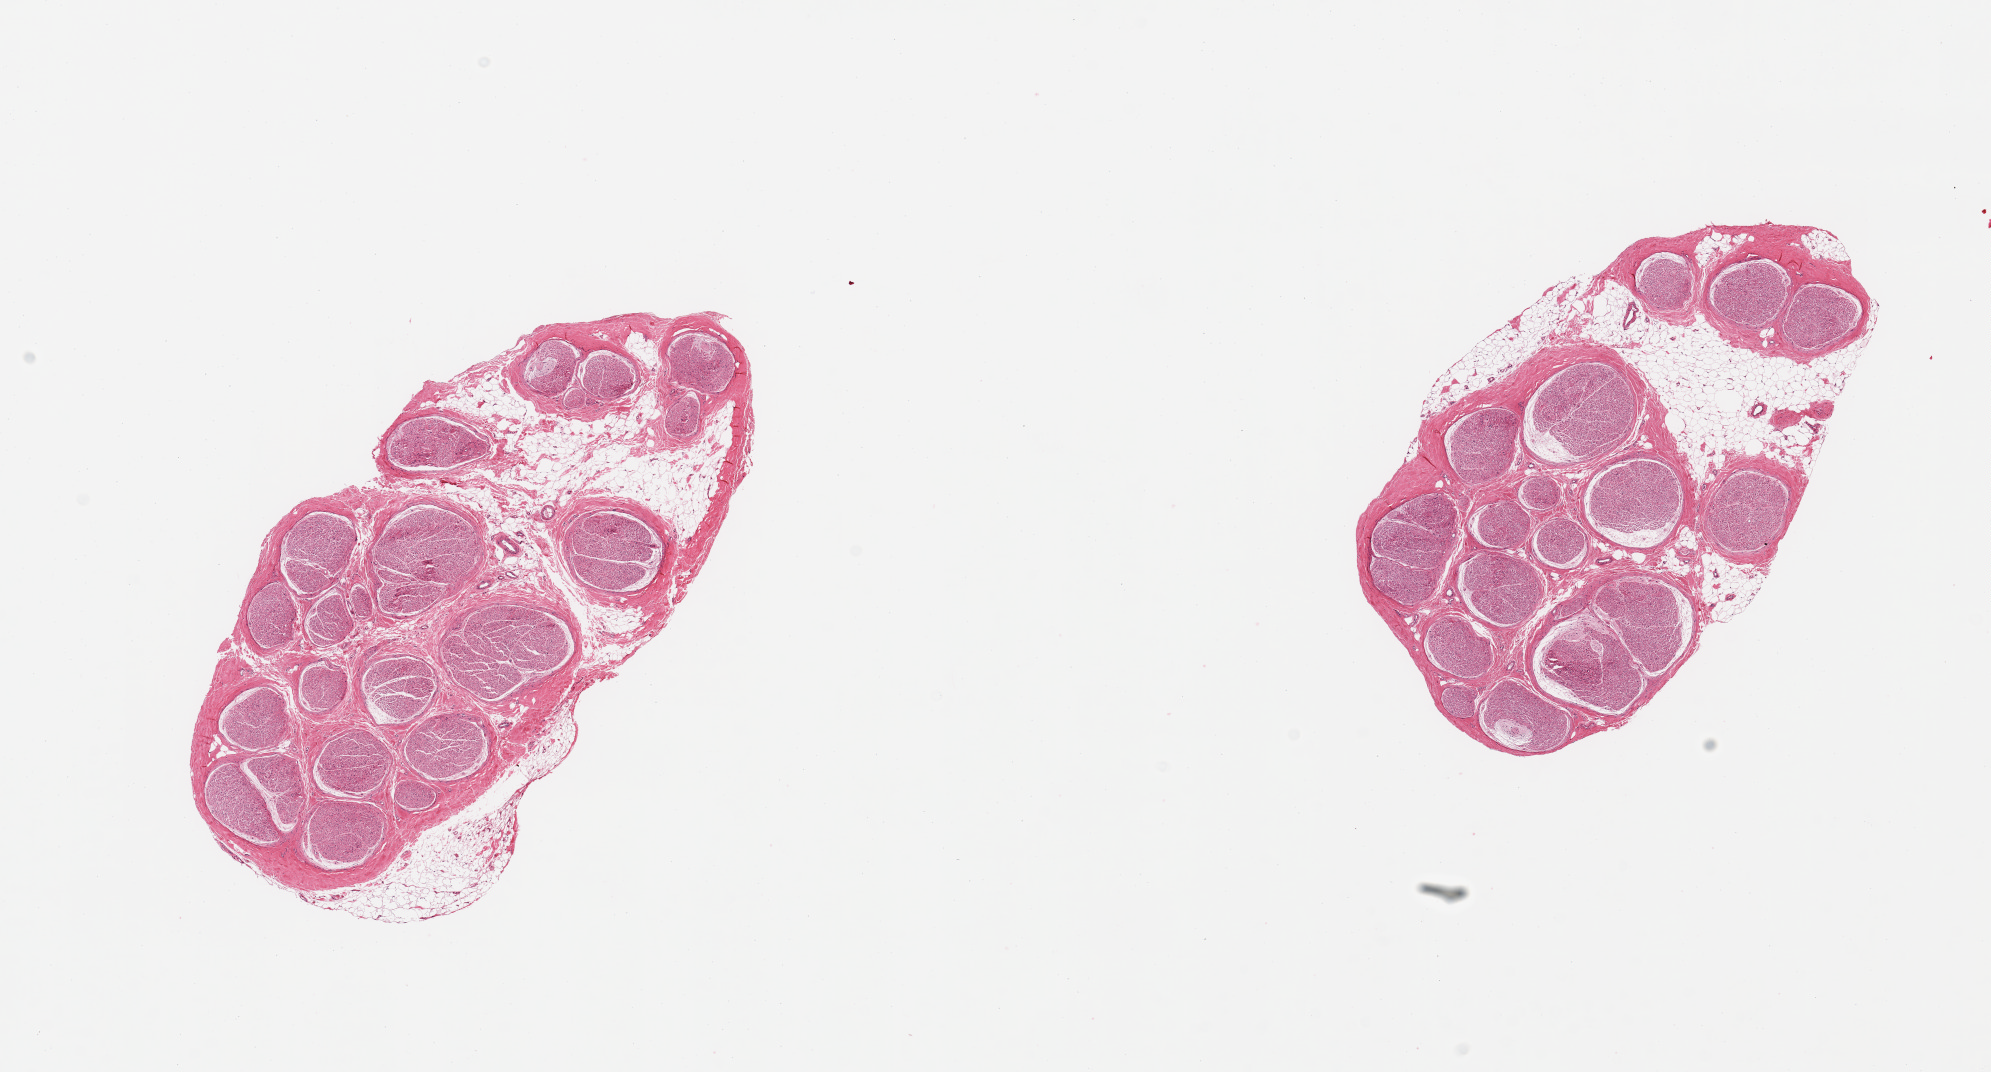
Hematoxylin and eosin (H&E) whole-slide image, brightfield, low-resolution overview of the scanned area, about 15.8 x 8.5 mm, PAXgene-fixed, paraffin-embedded tissue, target tissue: tibial nerve, donor tissue sample. Donor sex: female.
Review note (as recorded): 2 pieces; 20% internal fat.